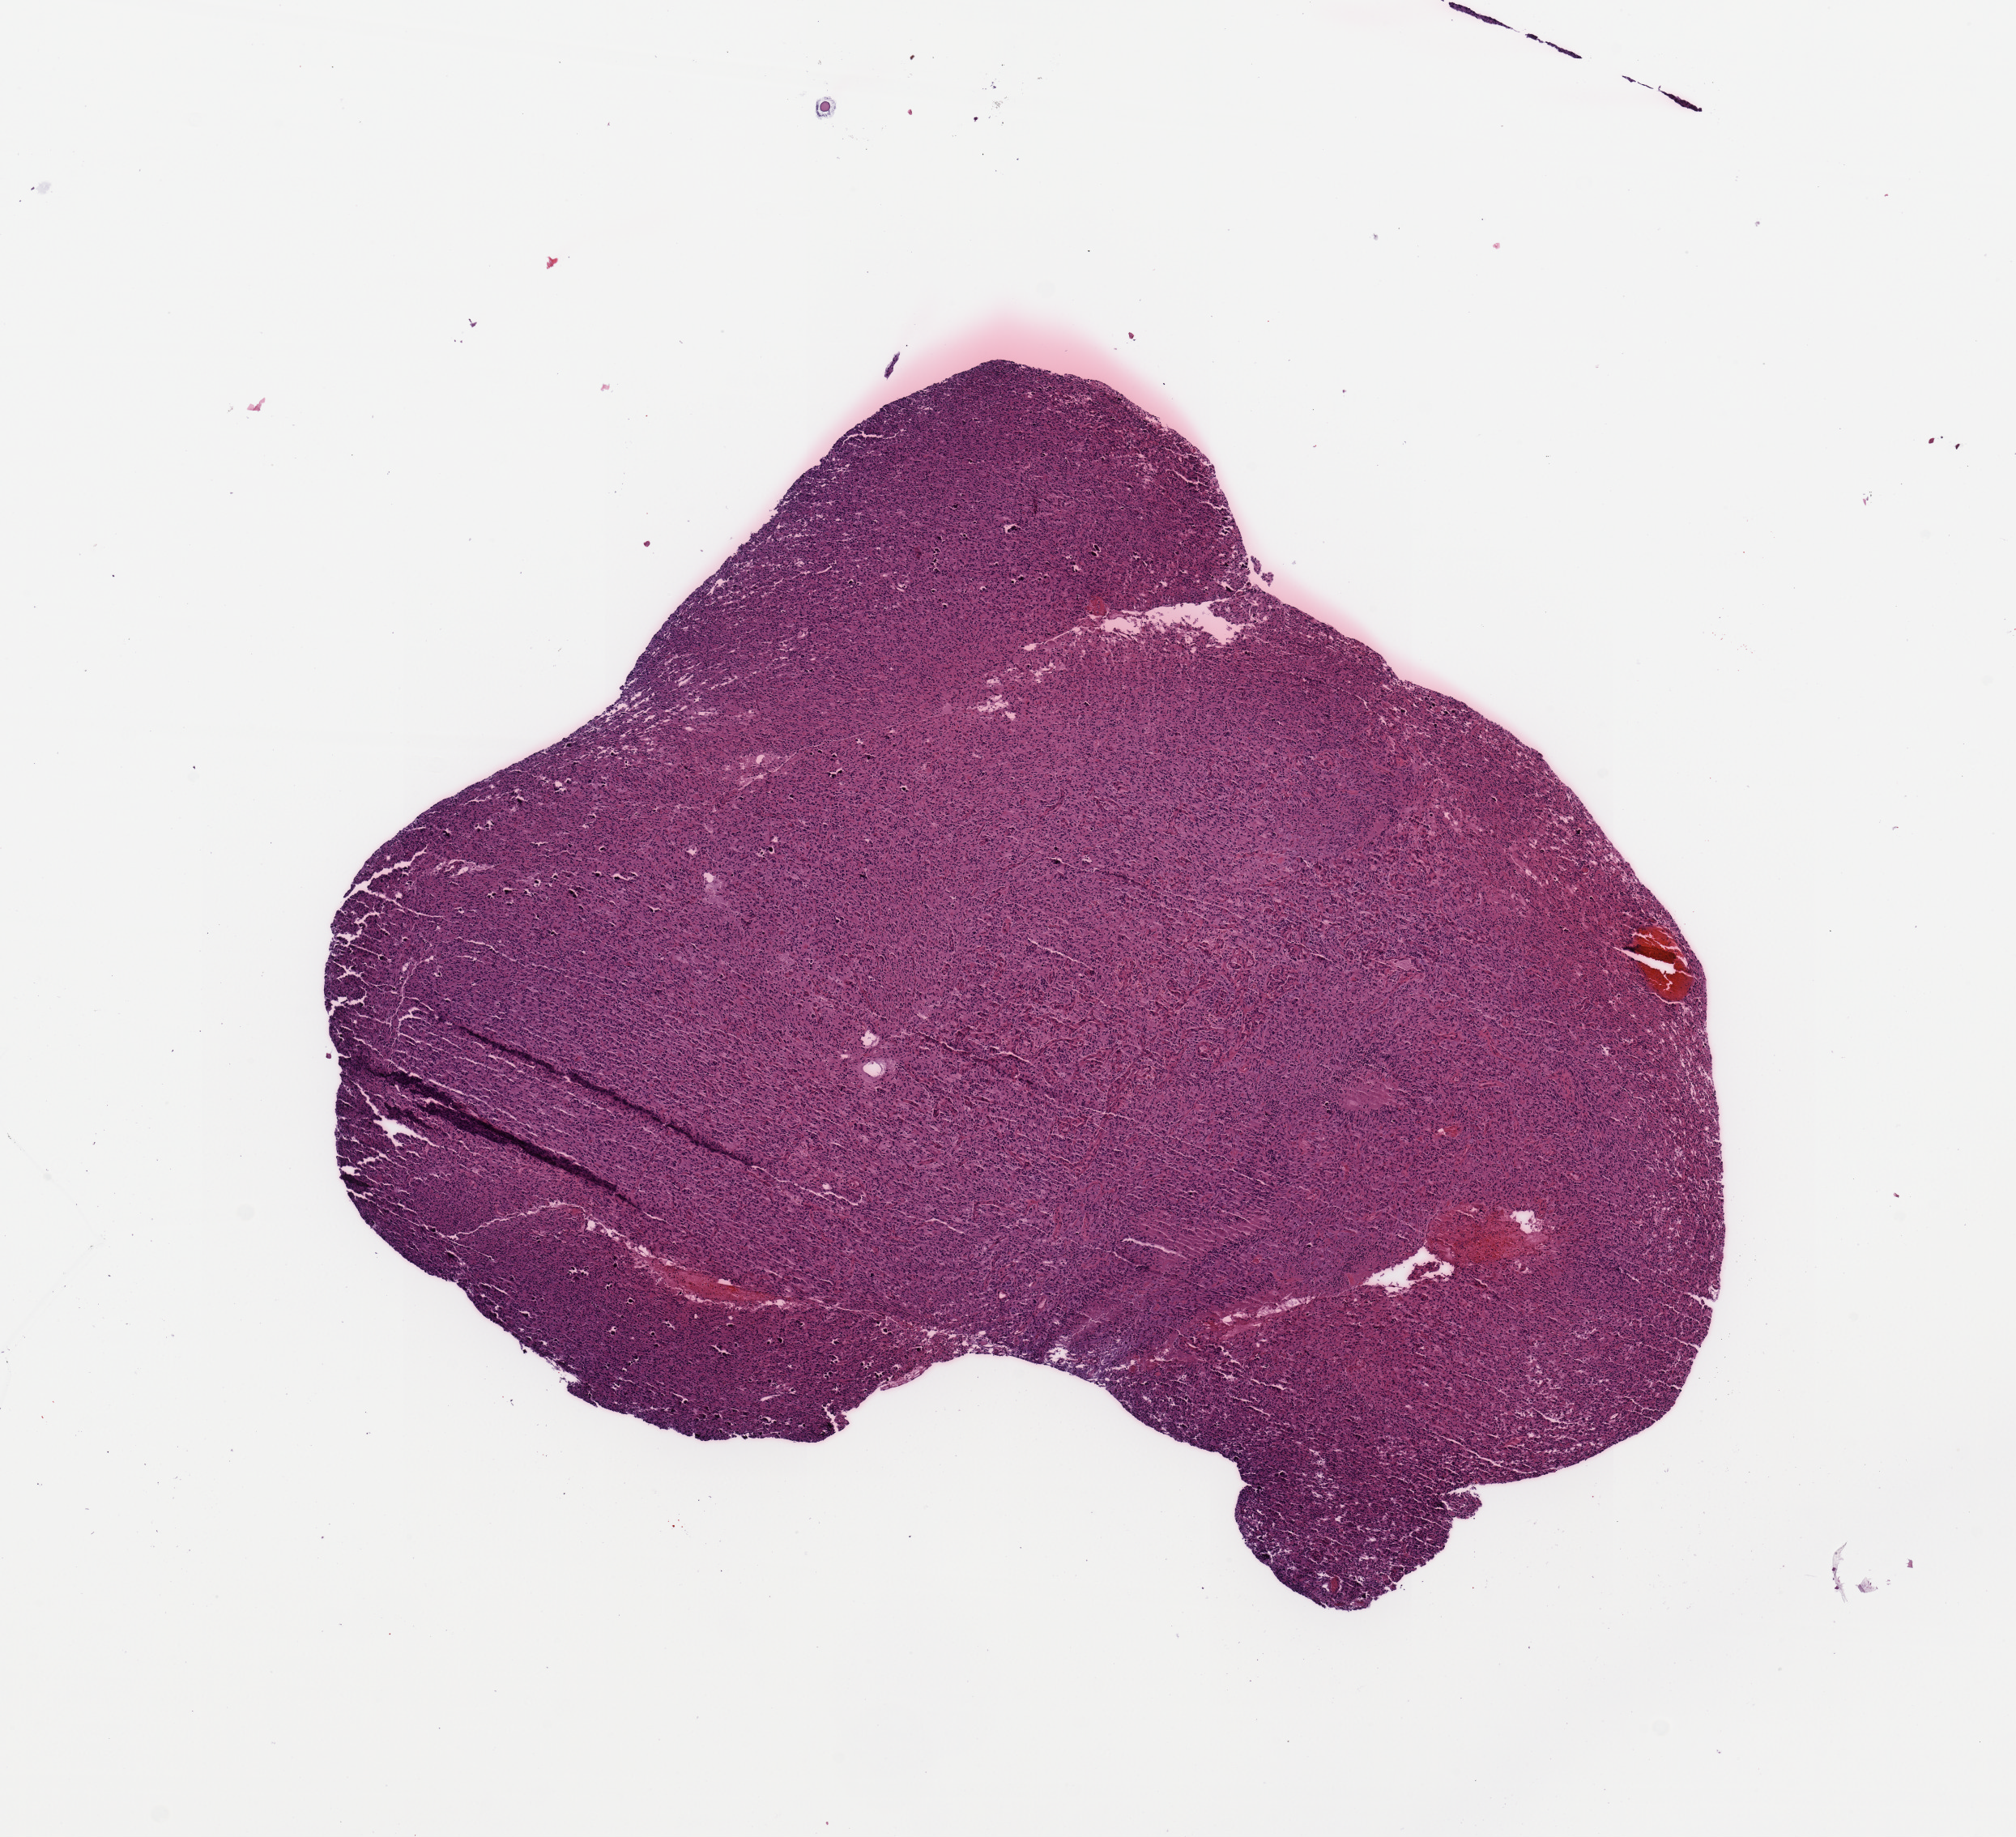
Whole-slide histology image, H&E-stained, whole scanned area (about 9.8 x 9.0 mm) shown as a low-resolution overview; tumour tissue sample, sampled site: frontal lobe. 59-year-old female patient. Composition of this section per pathologist review: tumour nuclei 90%, necrosis 5%.
• primary tumour site (as recorded): frontal lobe
• diagnosis: Glioblastoma